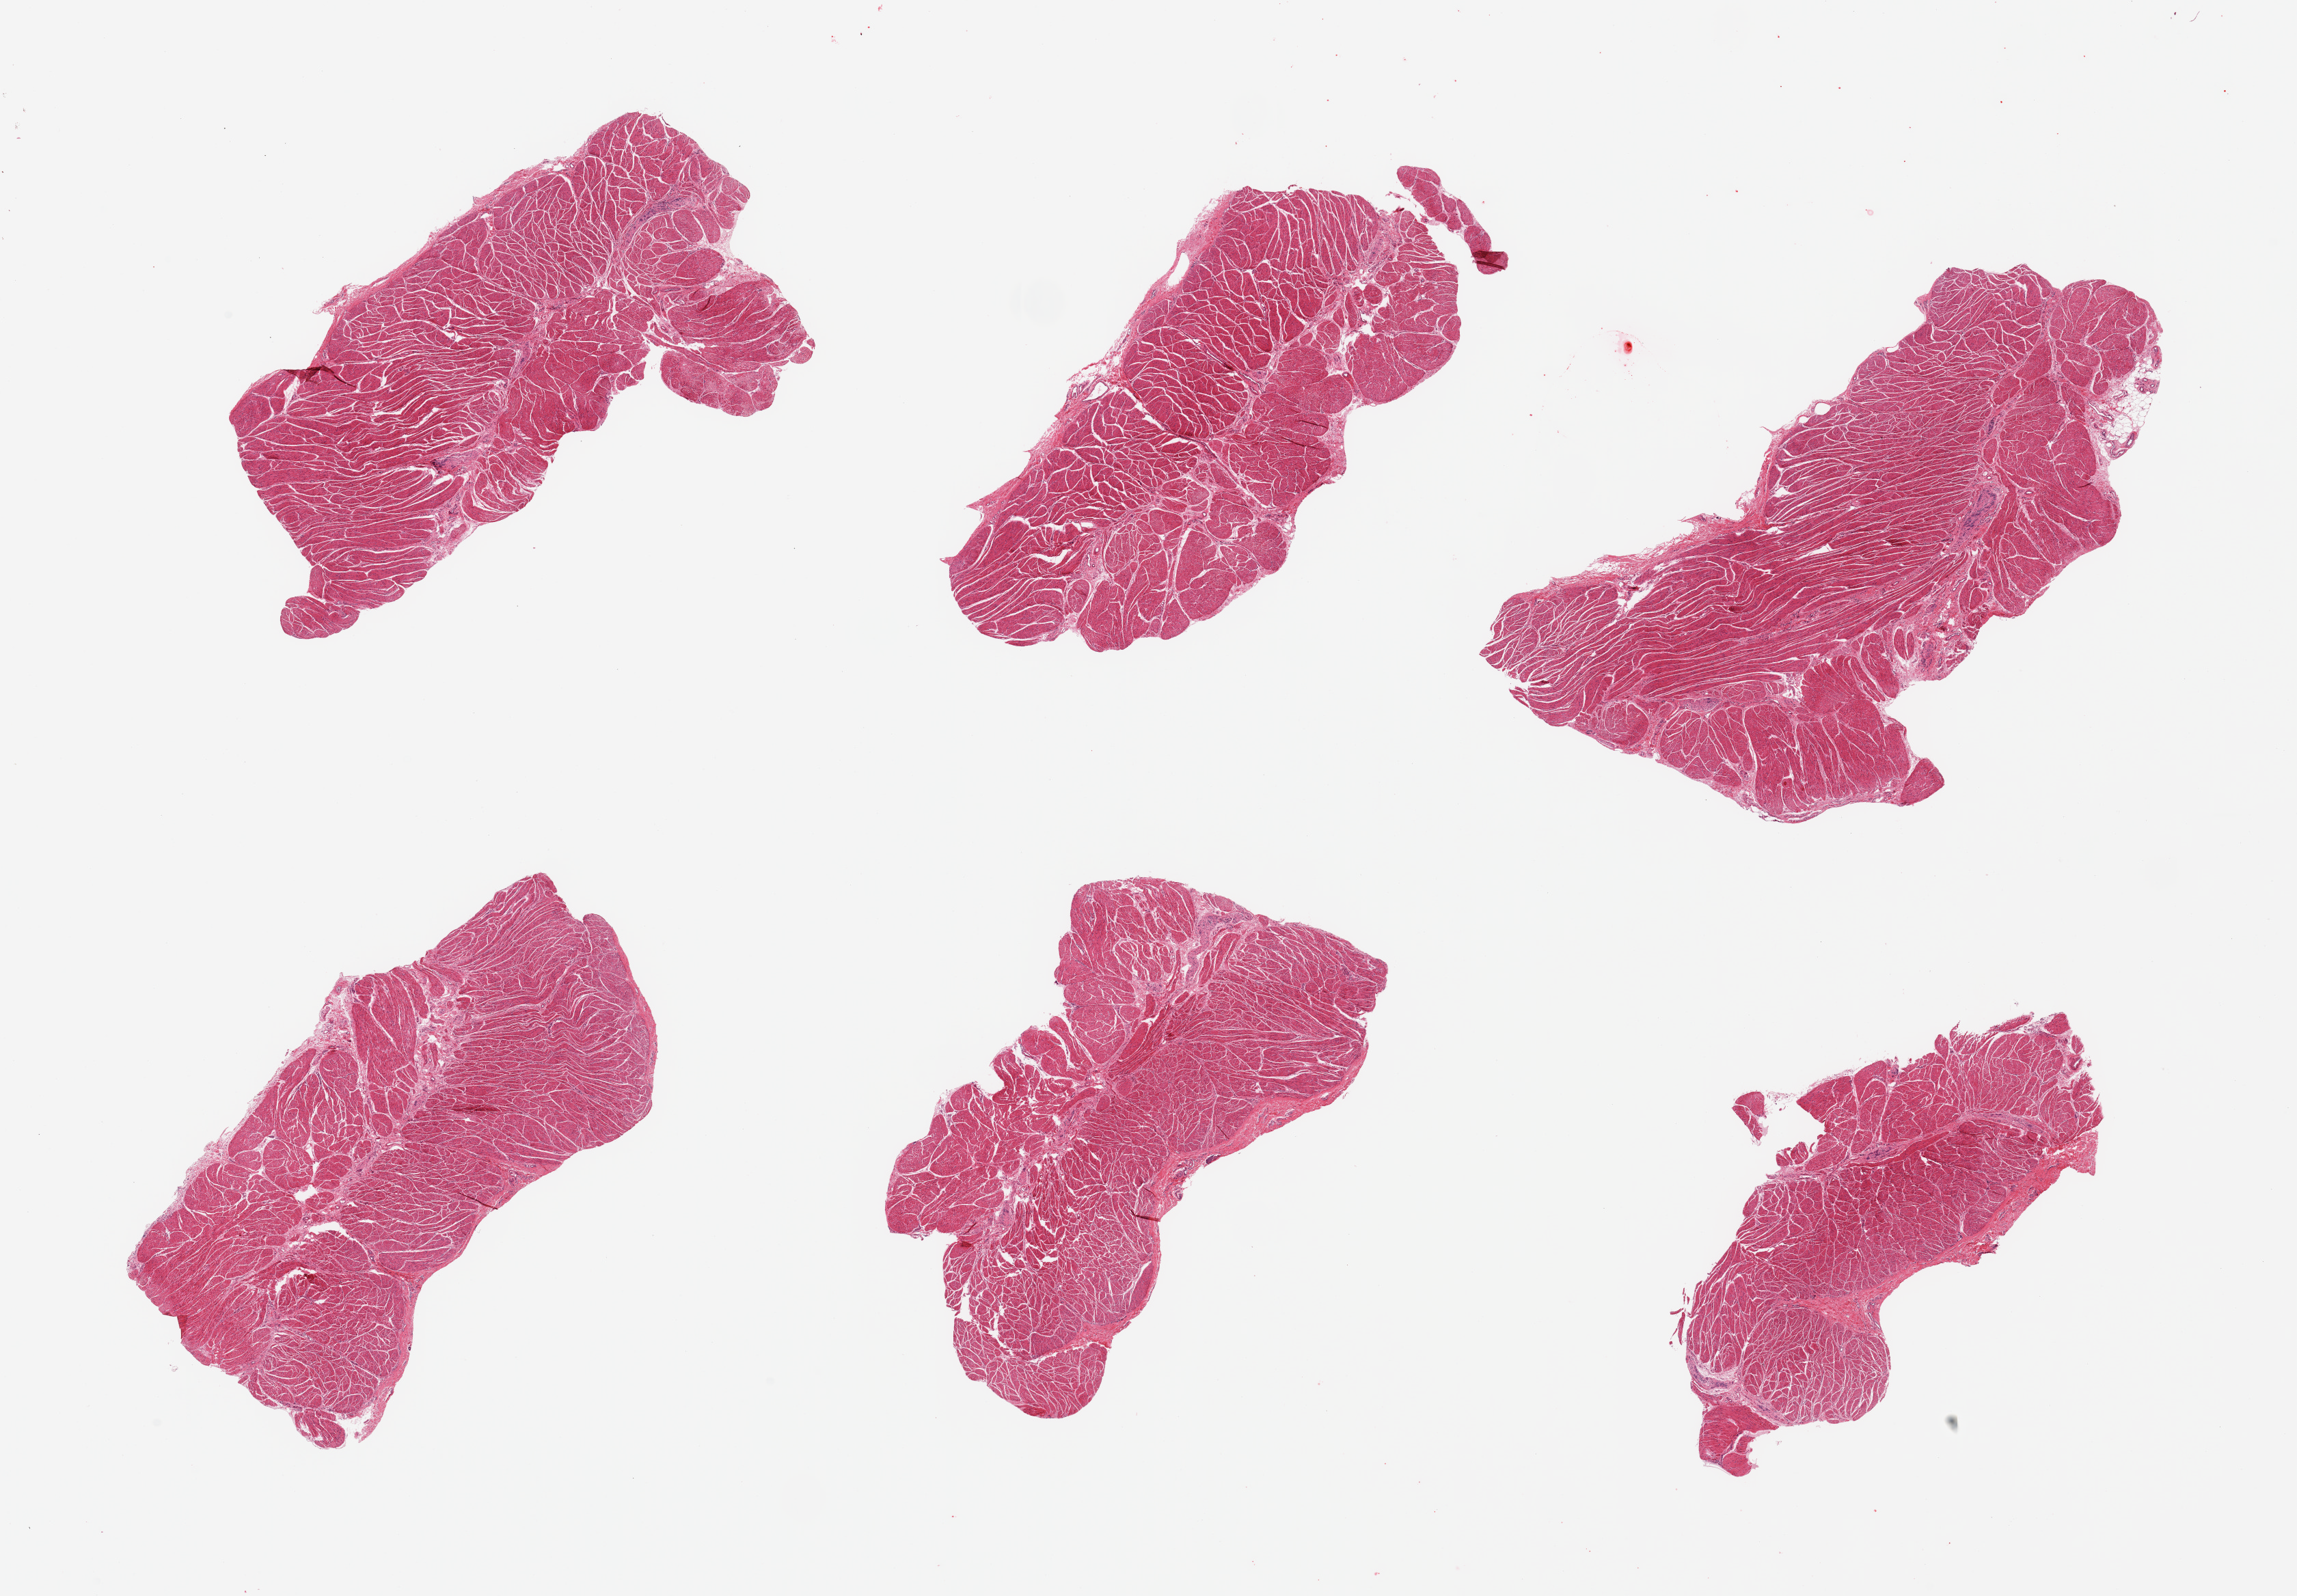
Whole-slide image, hematoxylin and eosin (H&E) stain — whole scanned area (about 26.6 x 18.5 mm, acquisition: 20x scan) shown as a low-resolution overview. PAXgene-fixed paraffin-embedded (PFPE) section. Section of esophageal muscle (target tissue). Tissue donor sample. Donor sex: male.
Pathologist's review note for this sample: 6 pieces; target muscularis.